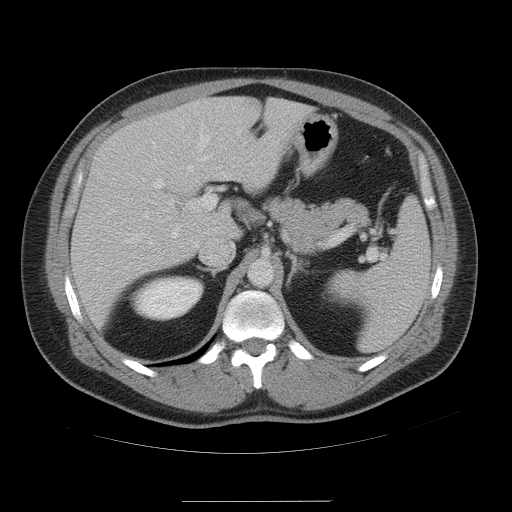
Contrast-enhanced abdominal CT, one axial slice. Slice 32 of 54 in the series (ordered by position). Intravenous contrast given. Soft-tissue window (W 400 / L 40 HU). 5 mm slice thickness. 512 × 512 image matrix. Male patient, age 40 years. Case-level facts recorded for this patient, not image findings: diagnosis: colorectal cancer liver metastases, imaged before liver resection; multiple liver metastases: no; largest metastasis: 15 cm.
Annotated regions visible in this slice (expert manual segmentation):
- hepatic veins: box from (x=132, y=128) to (x=211, y=244) px
- liver: (x=71, y=96)–(x=314, y=329)
- planned liver remnant (the part of the liver to remain after resection): (x=197, y=96)–(x=314, y=238)
- portal vein (with intrahepatic branches): (x=146, y=180)–(x=218, y=238)